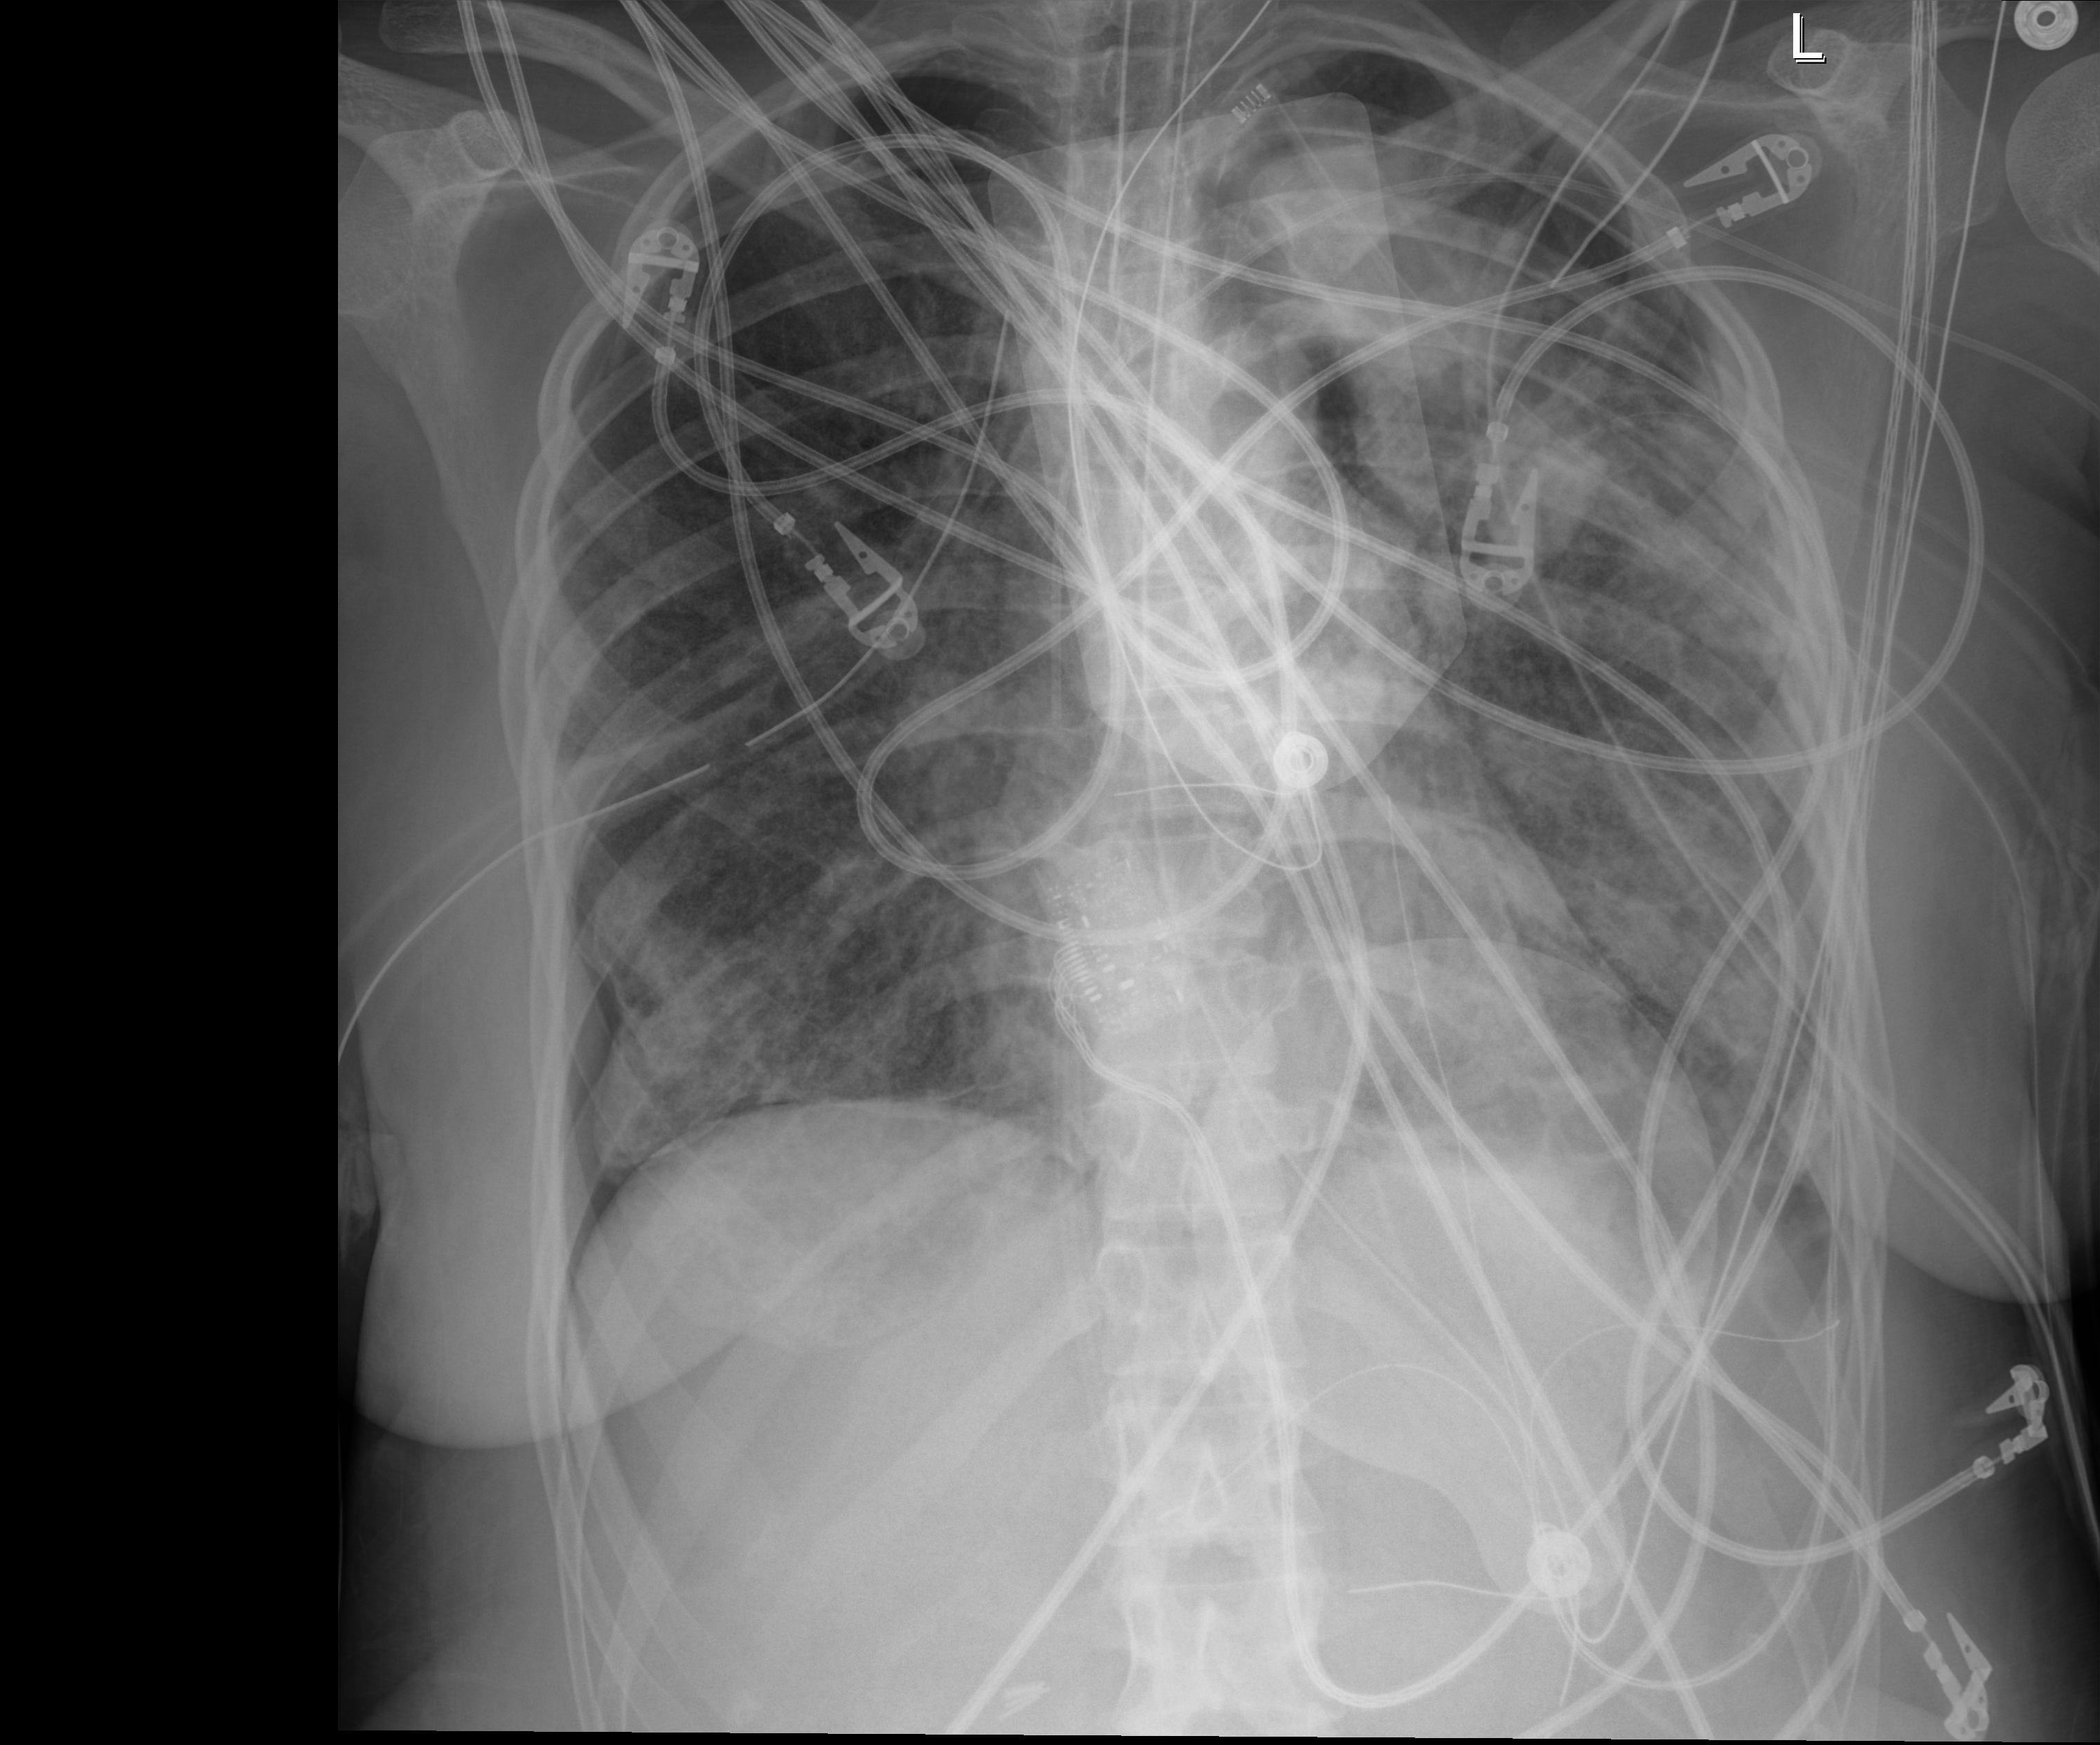
Bedside chest radiograph (digital radiography), anteroposterior (AP) projection. Patient hospitalised with COVID-19, aged 18–59 years.
Admission-level facts for this patient (not findings on this image; timing relative to this image not recorded):
- diabetes (admission record): no